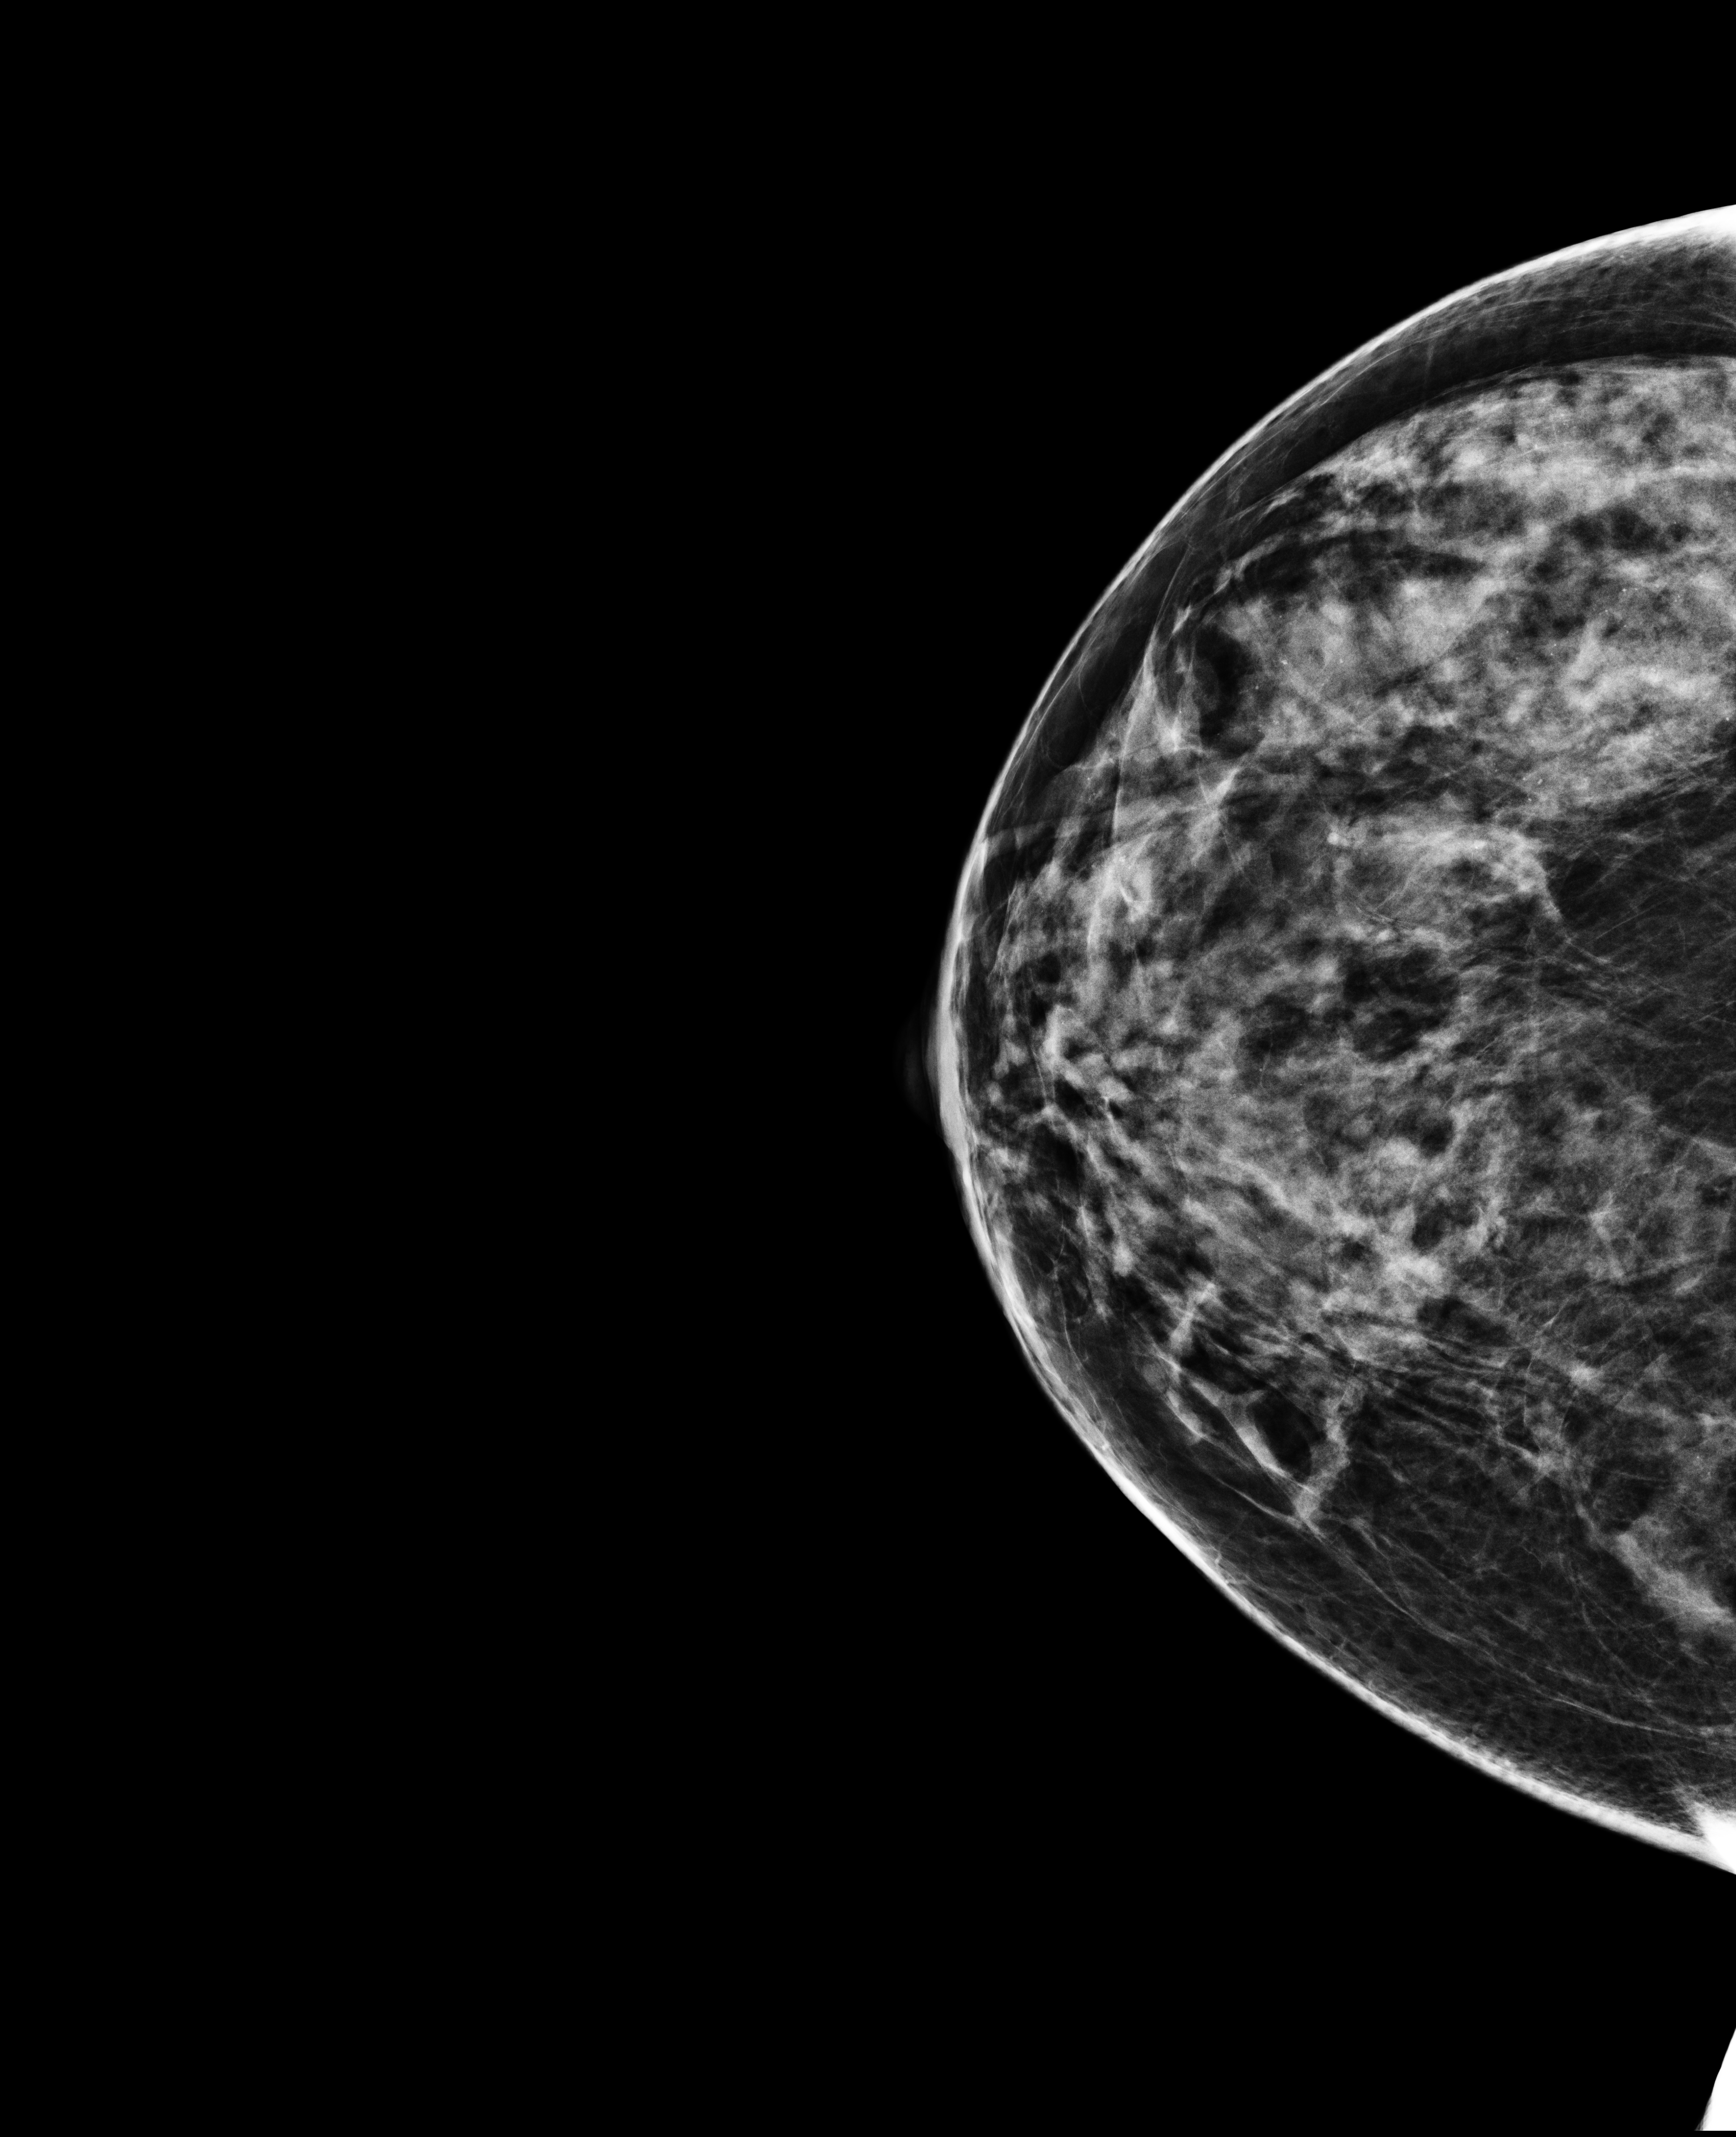
Full-field digital mammogram (FFDM), right breast, CC view, annual screening mammography examination, compressed breast thickness 58 mm. Female patient, age 51 years.
- BI-RADS breast density category at the screening exam (both breasts, scale 1–4): 3
- final BI-RADS category for the screening round (tomosynthesis exam, both breasts): category 1
- recall: no recall after this screen